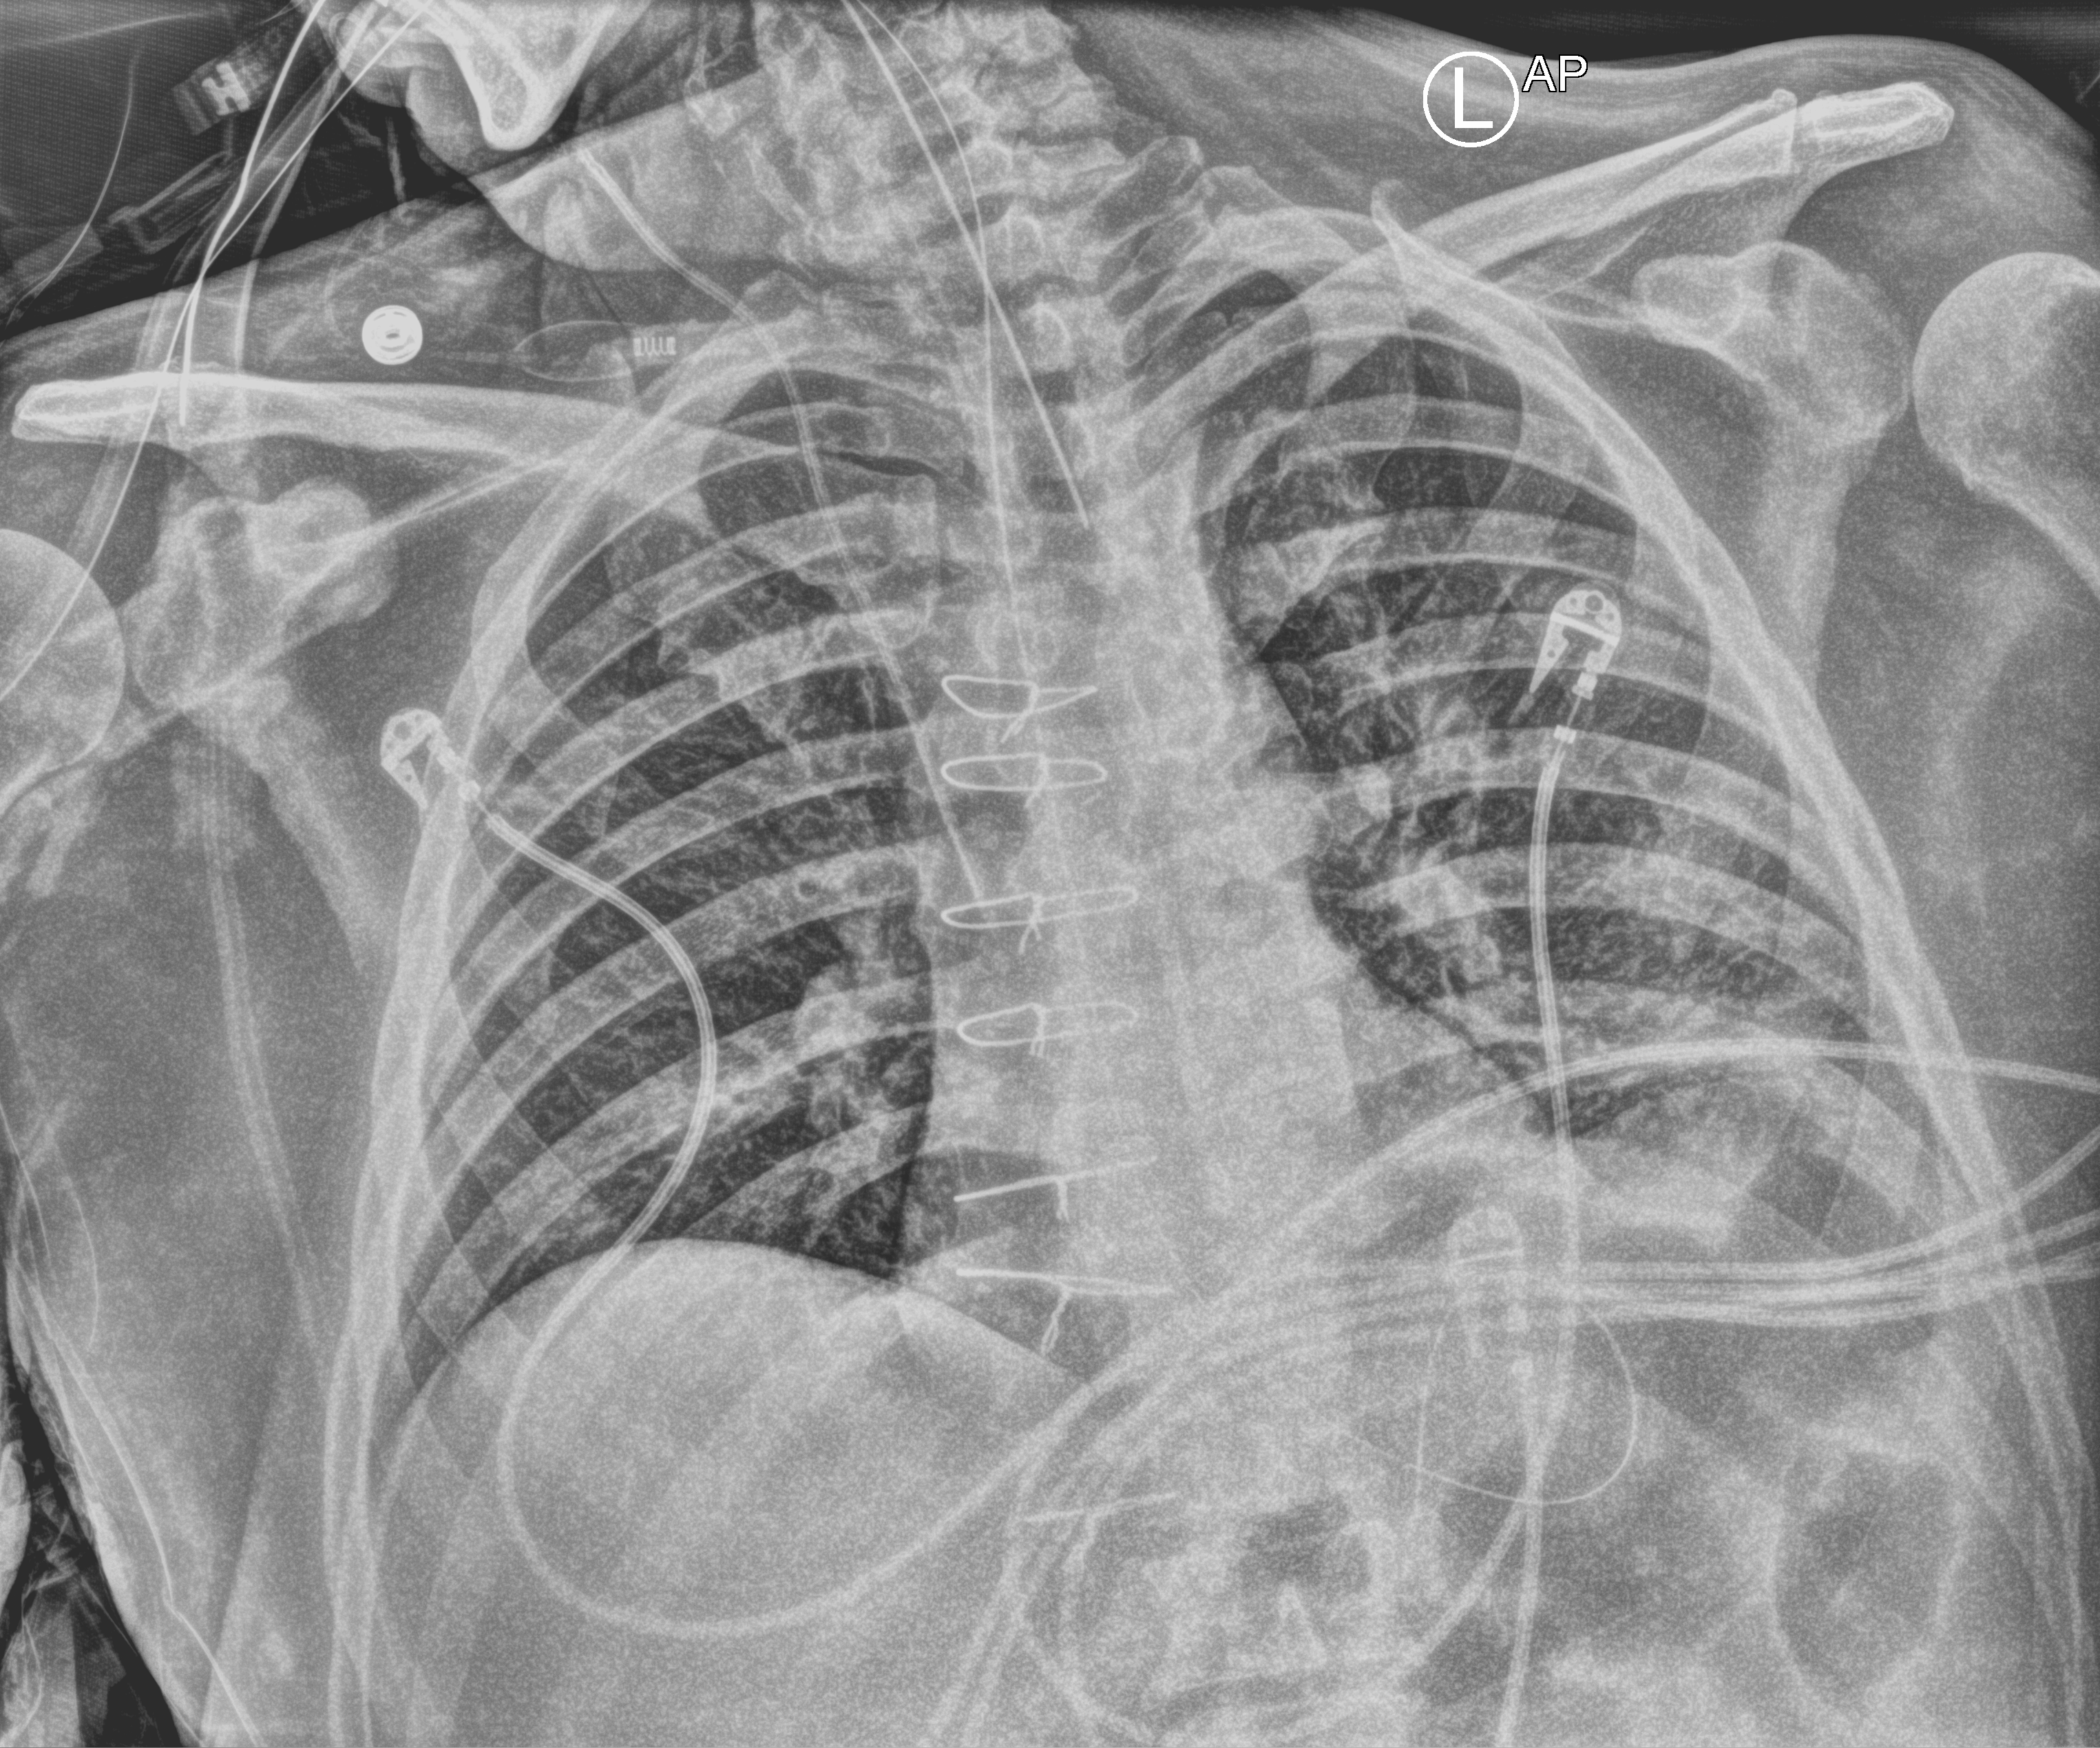
Bedside chest radiograph (computed radiography), anteroposterior (AP) projection. Patient hospitalised with COVID-19; male, aged 60–74 years.
From the hospital-stay record, not from the radiograph (when in the stay this image was taken is not recorded): smoking status (admission record): former.